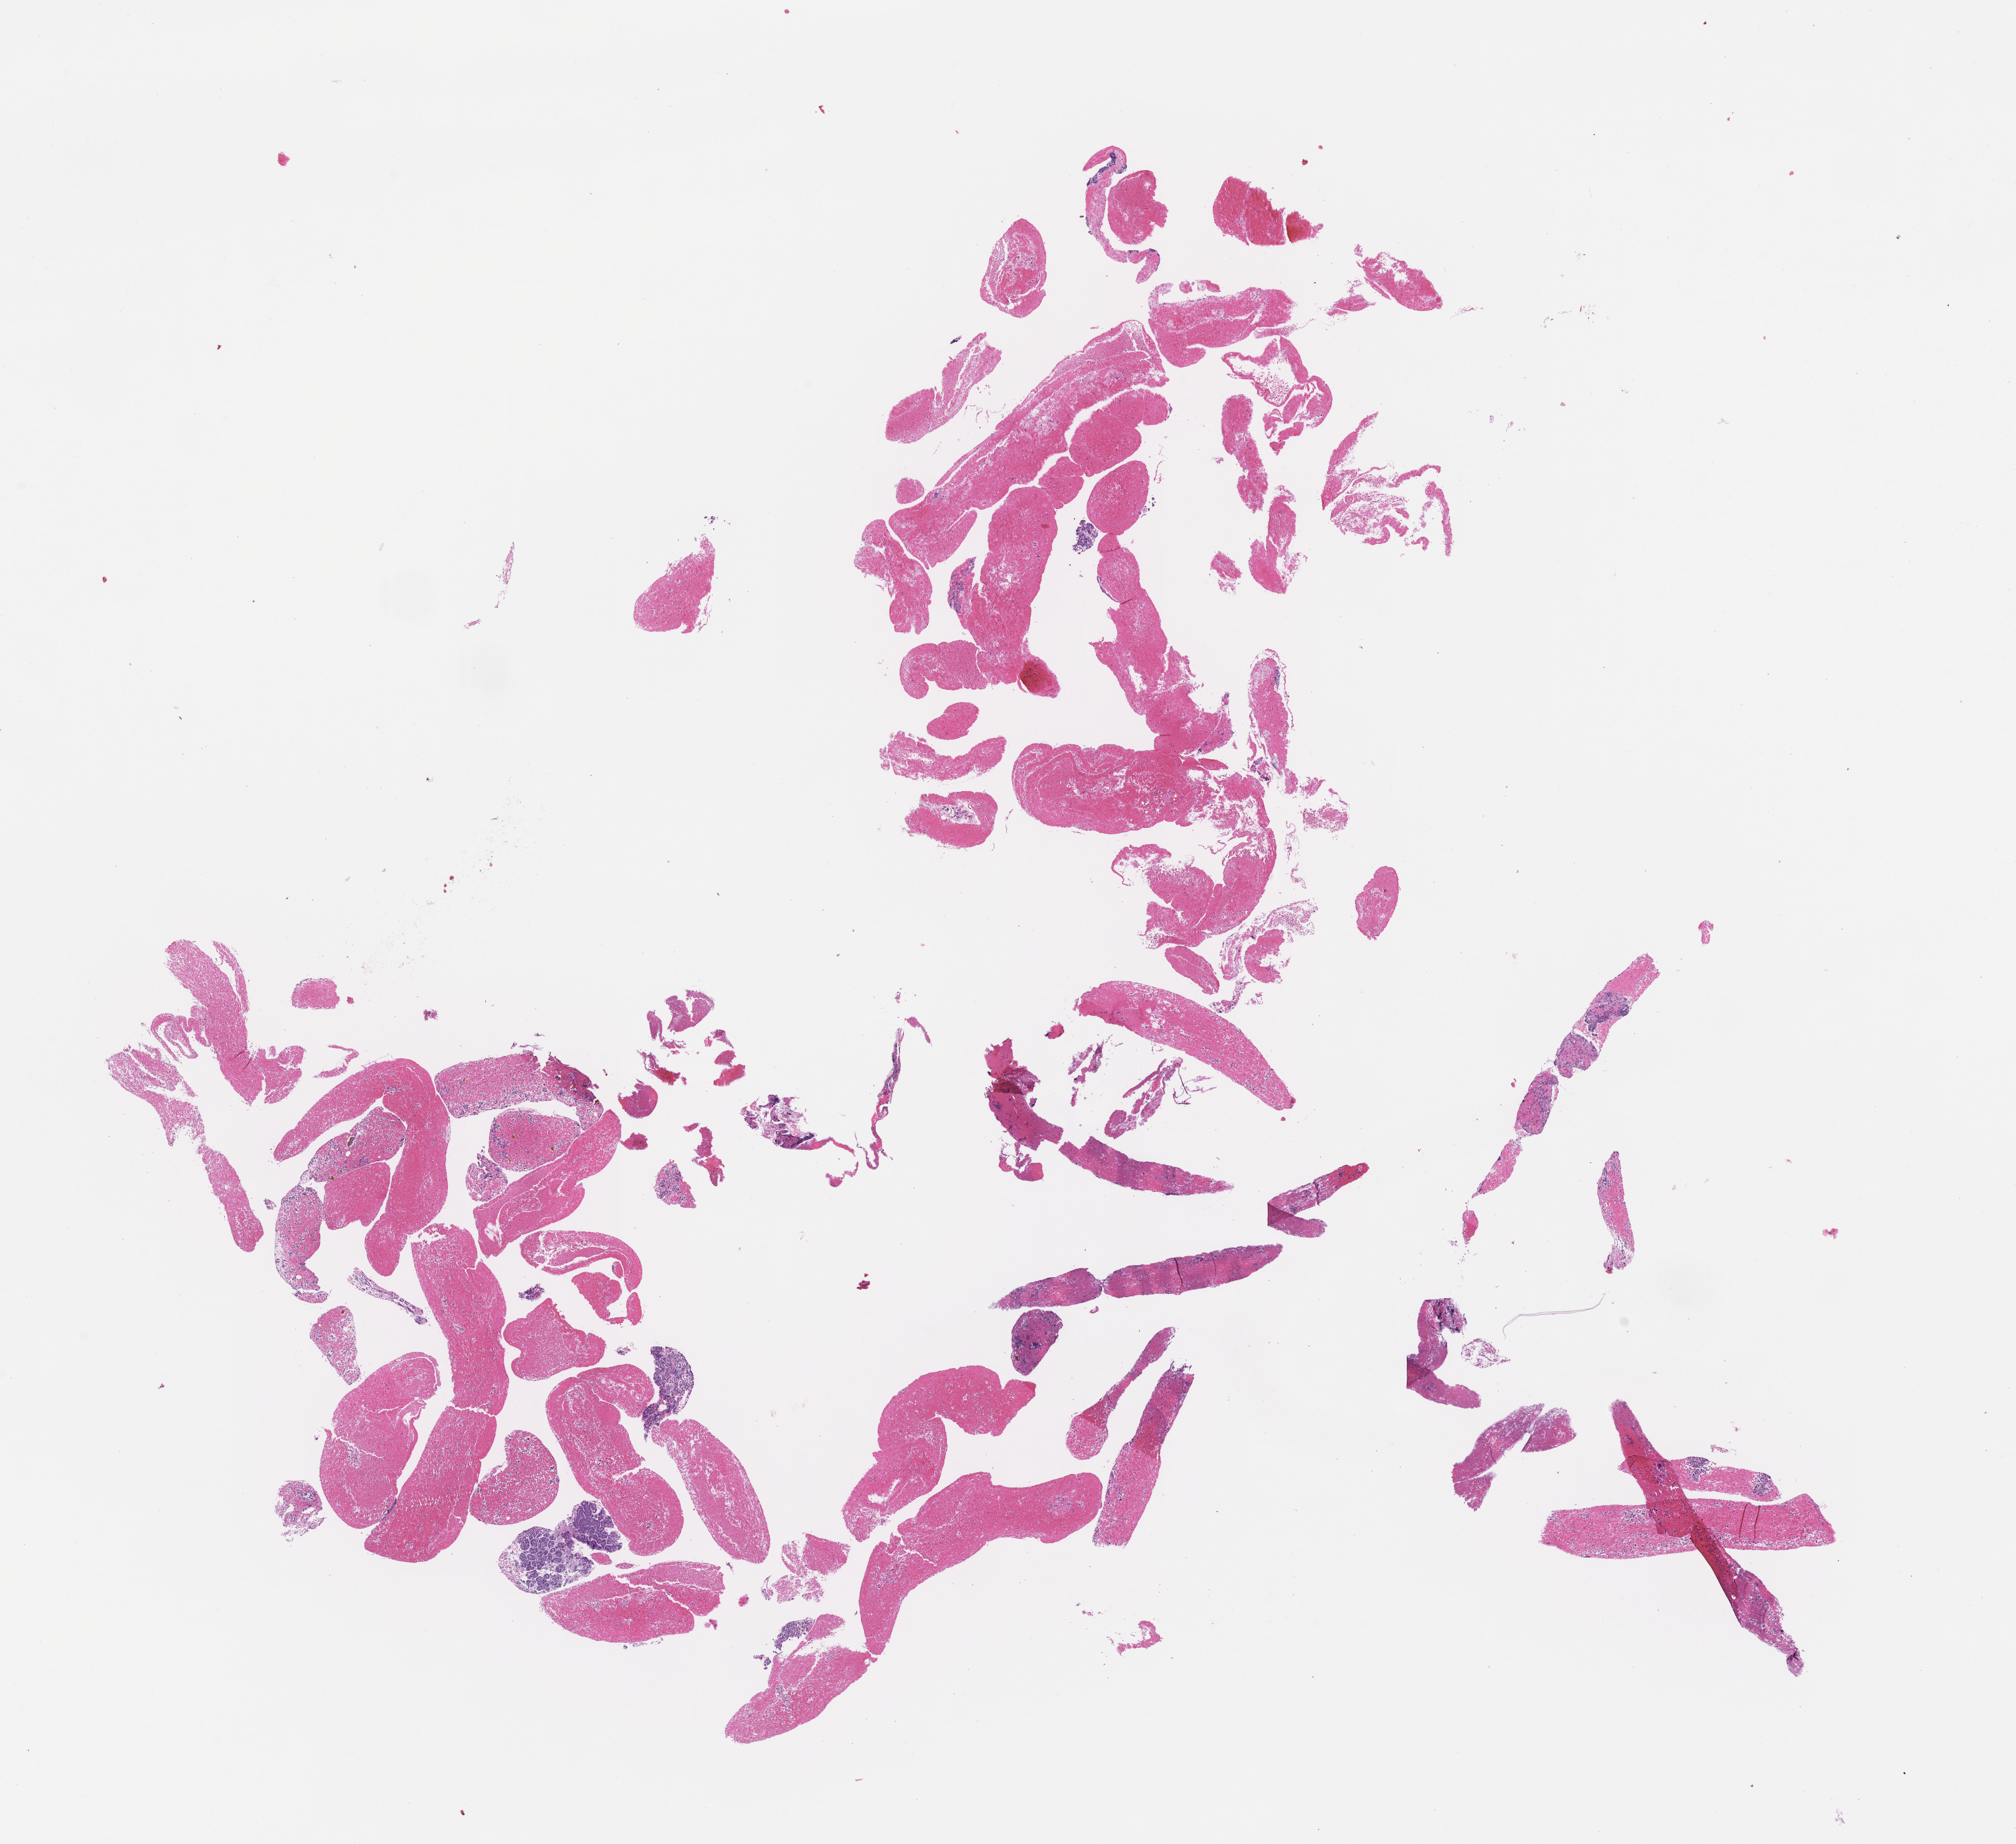
Digitized H&E-stained section — a low-resolution overview of the entire scanned area, about 13.1 x 12.0 mm. Formalin-fixed, paraffin-embedded (FFPE) tissue. Patient sex: female.
• this section: metastatic tumor tissue
• patient diagnosis (primary): Adenocarcinoma of the Gastroesophageal Junction